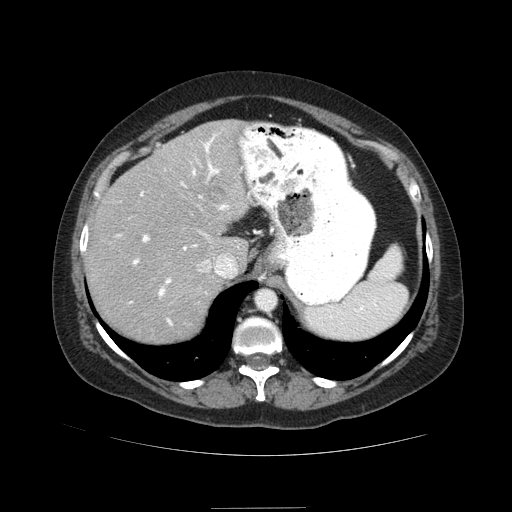
Contrast-enhanced abdominal CT (liver protocol), one axial slice. Position 65 of 89 along the scan axis. Reconstruction kernel STANDARD. 120 kVp. Soft-tissue window (W 400 / L 40 HU). 512 × 512 image matrix. Case-level facts recorded for this patient, not image findings: diagnosis: hepatocellular carcinoma (patient treated with transarterial chemoembolisation; whether this scan precedes or follows treatment is not stated here); TNM stage (as recorded): Stage-IIIB; Child-Pugh class: A; tumour nodularity: multinodular.
Annotated regions visible in this slice (semi-automatic segmentation, software-assisted and operator-edited):
- abdominal aorta: bounding box (x1, y1, x2, y2) in pixels: (257, 290, 276, 309)
- liver parenchyma outside the tumour (the mass and vessels are separate outlines, so this box may not span the whole liver): (86, 120, 252, 342)
- liver vessels: (117, 134, 229, 326)